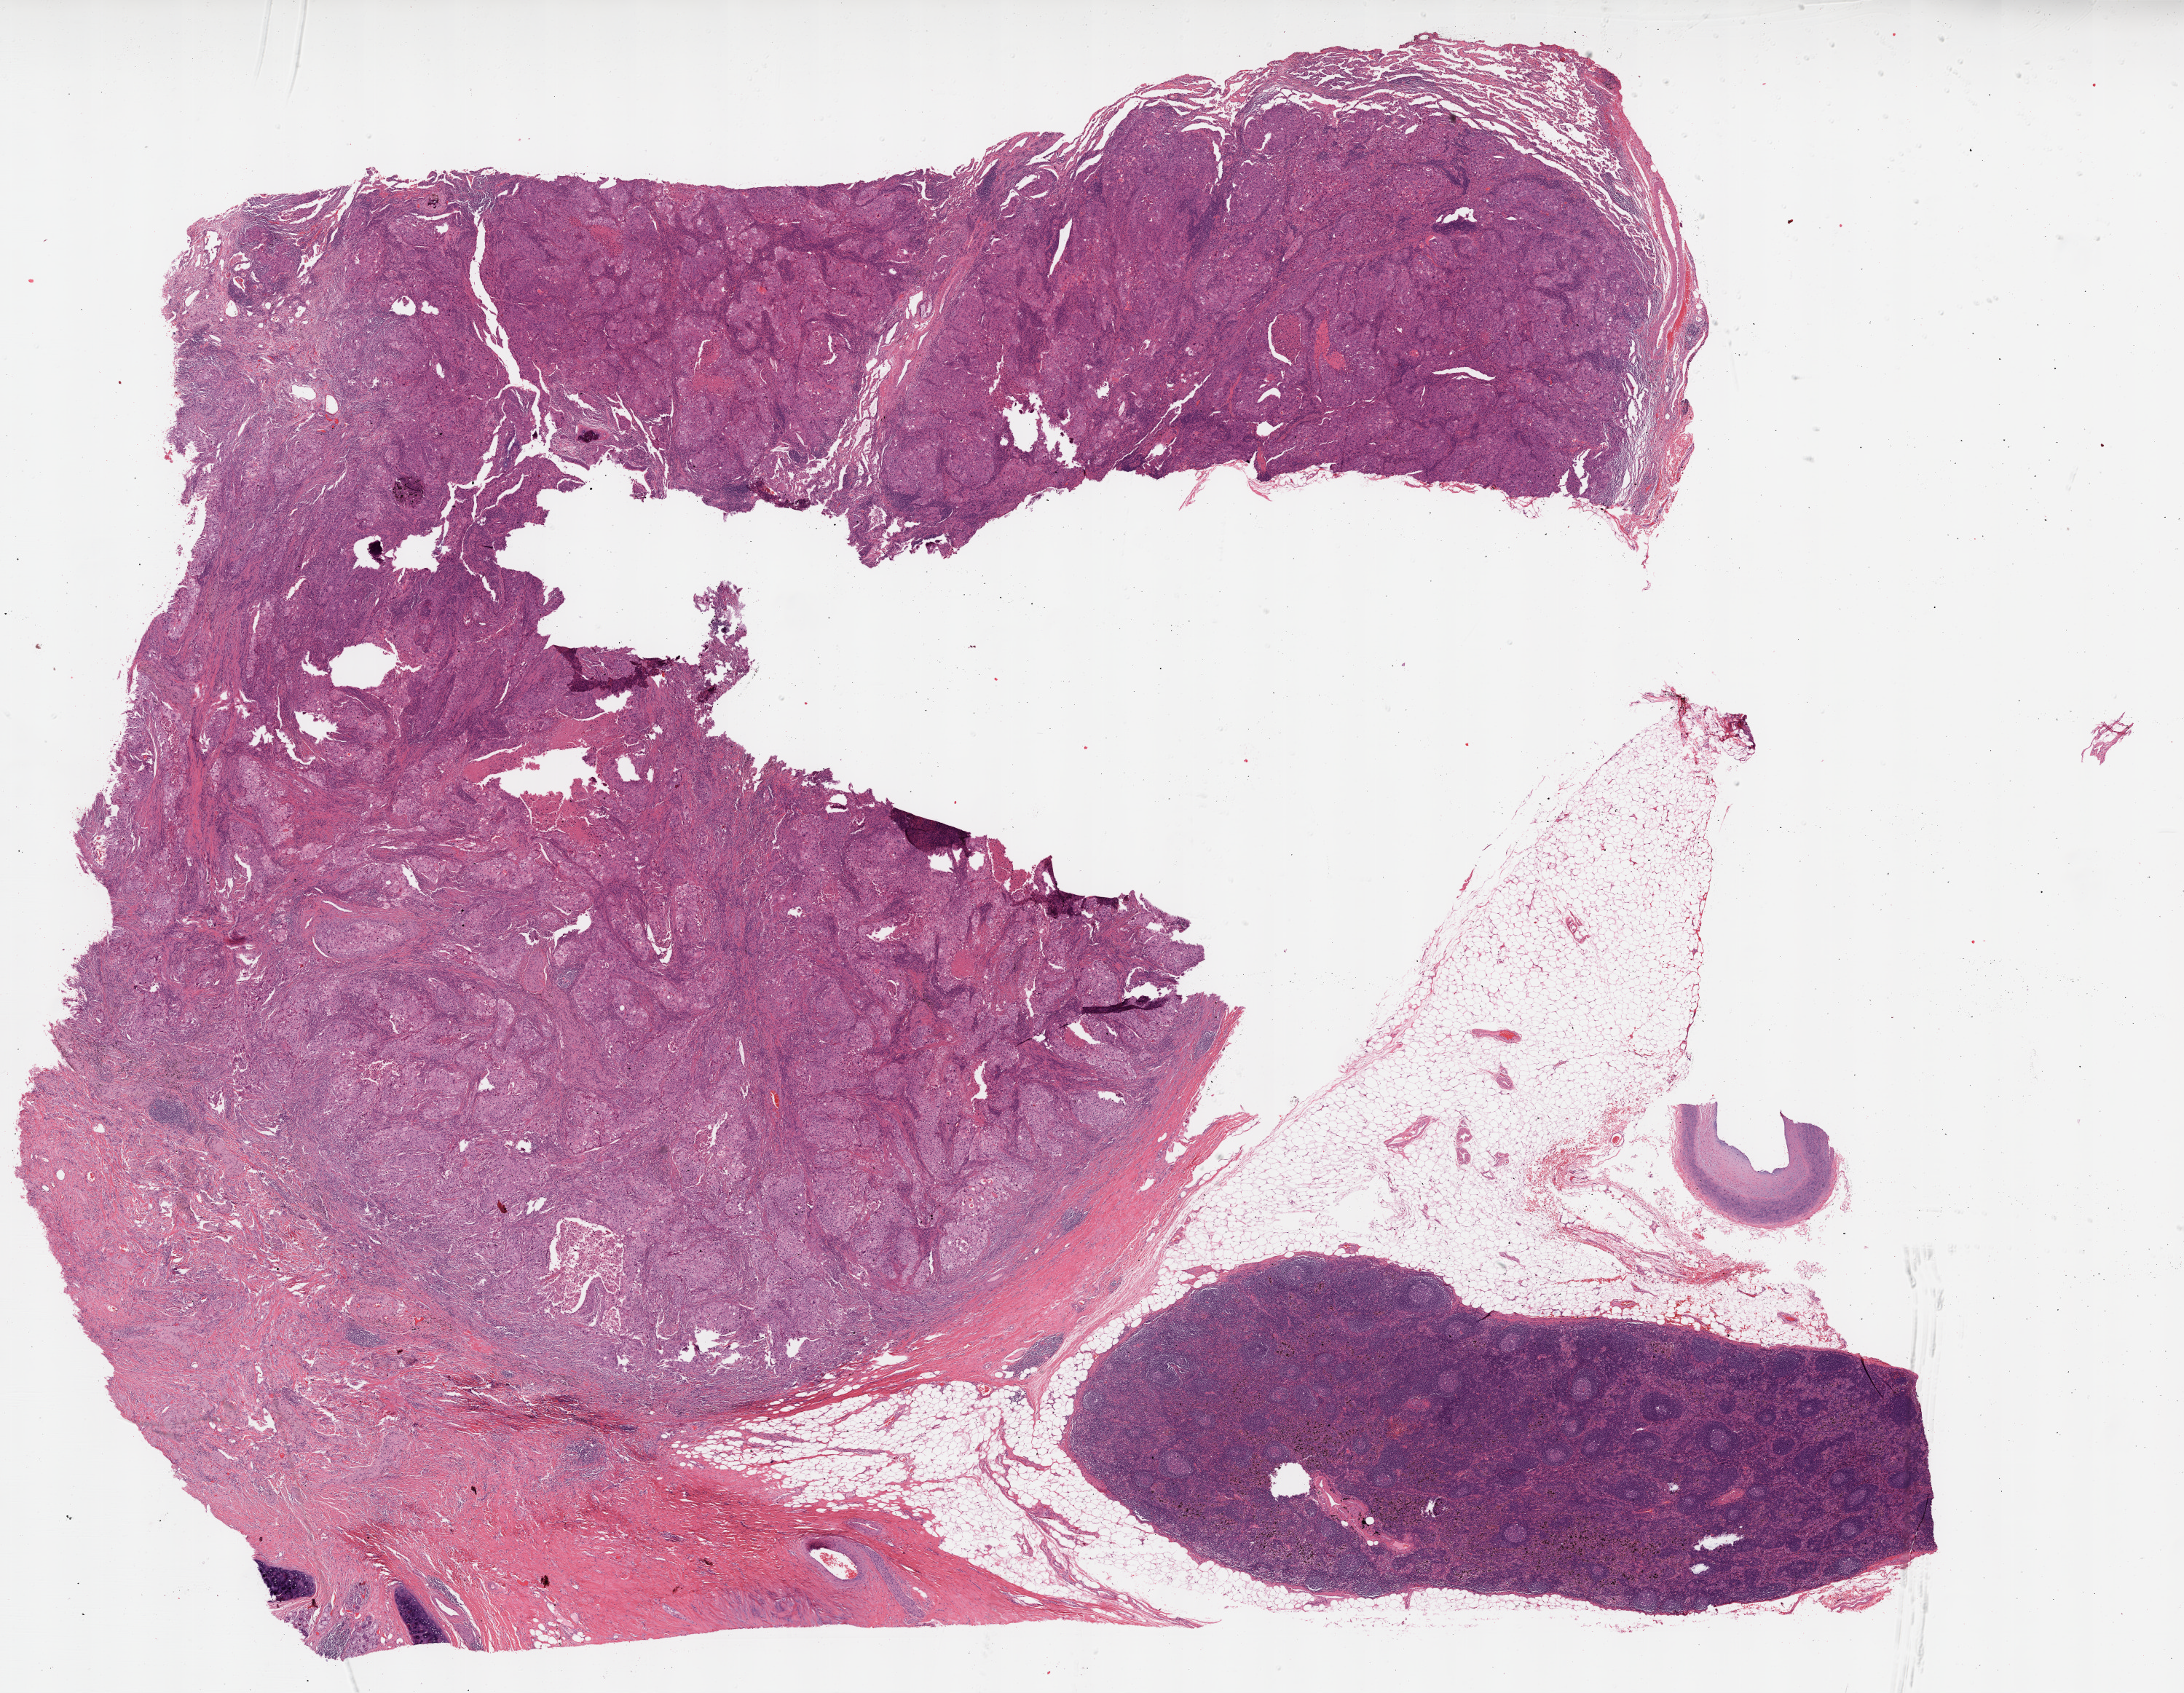
Digitized Hematoxylin and eosin (H&E) stained tissue section (whole slide) — low-resolution overview of the scanned area, about 24.1 x 18.7 mm (from a 20x scan); FFPE section; lung, primary tumour sample. Female patient; age at initial diagnosis 66 years.
Diagnosis: Squamous cell carcinoma, NOS. Laterality: right. AJCC pathologic stage: IIB (6th edition).